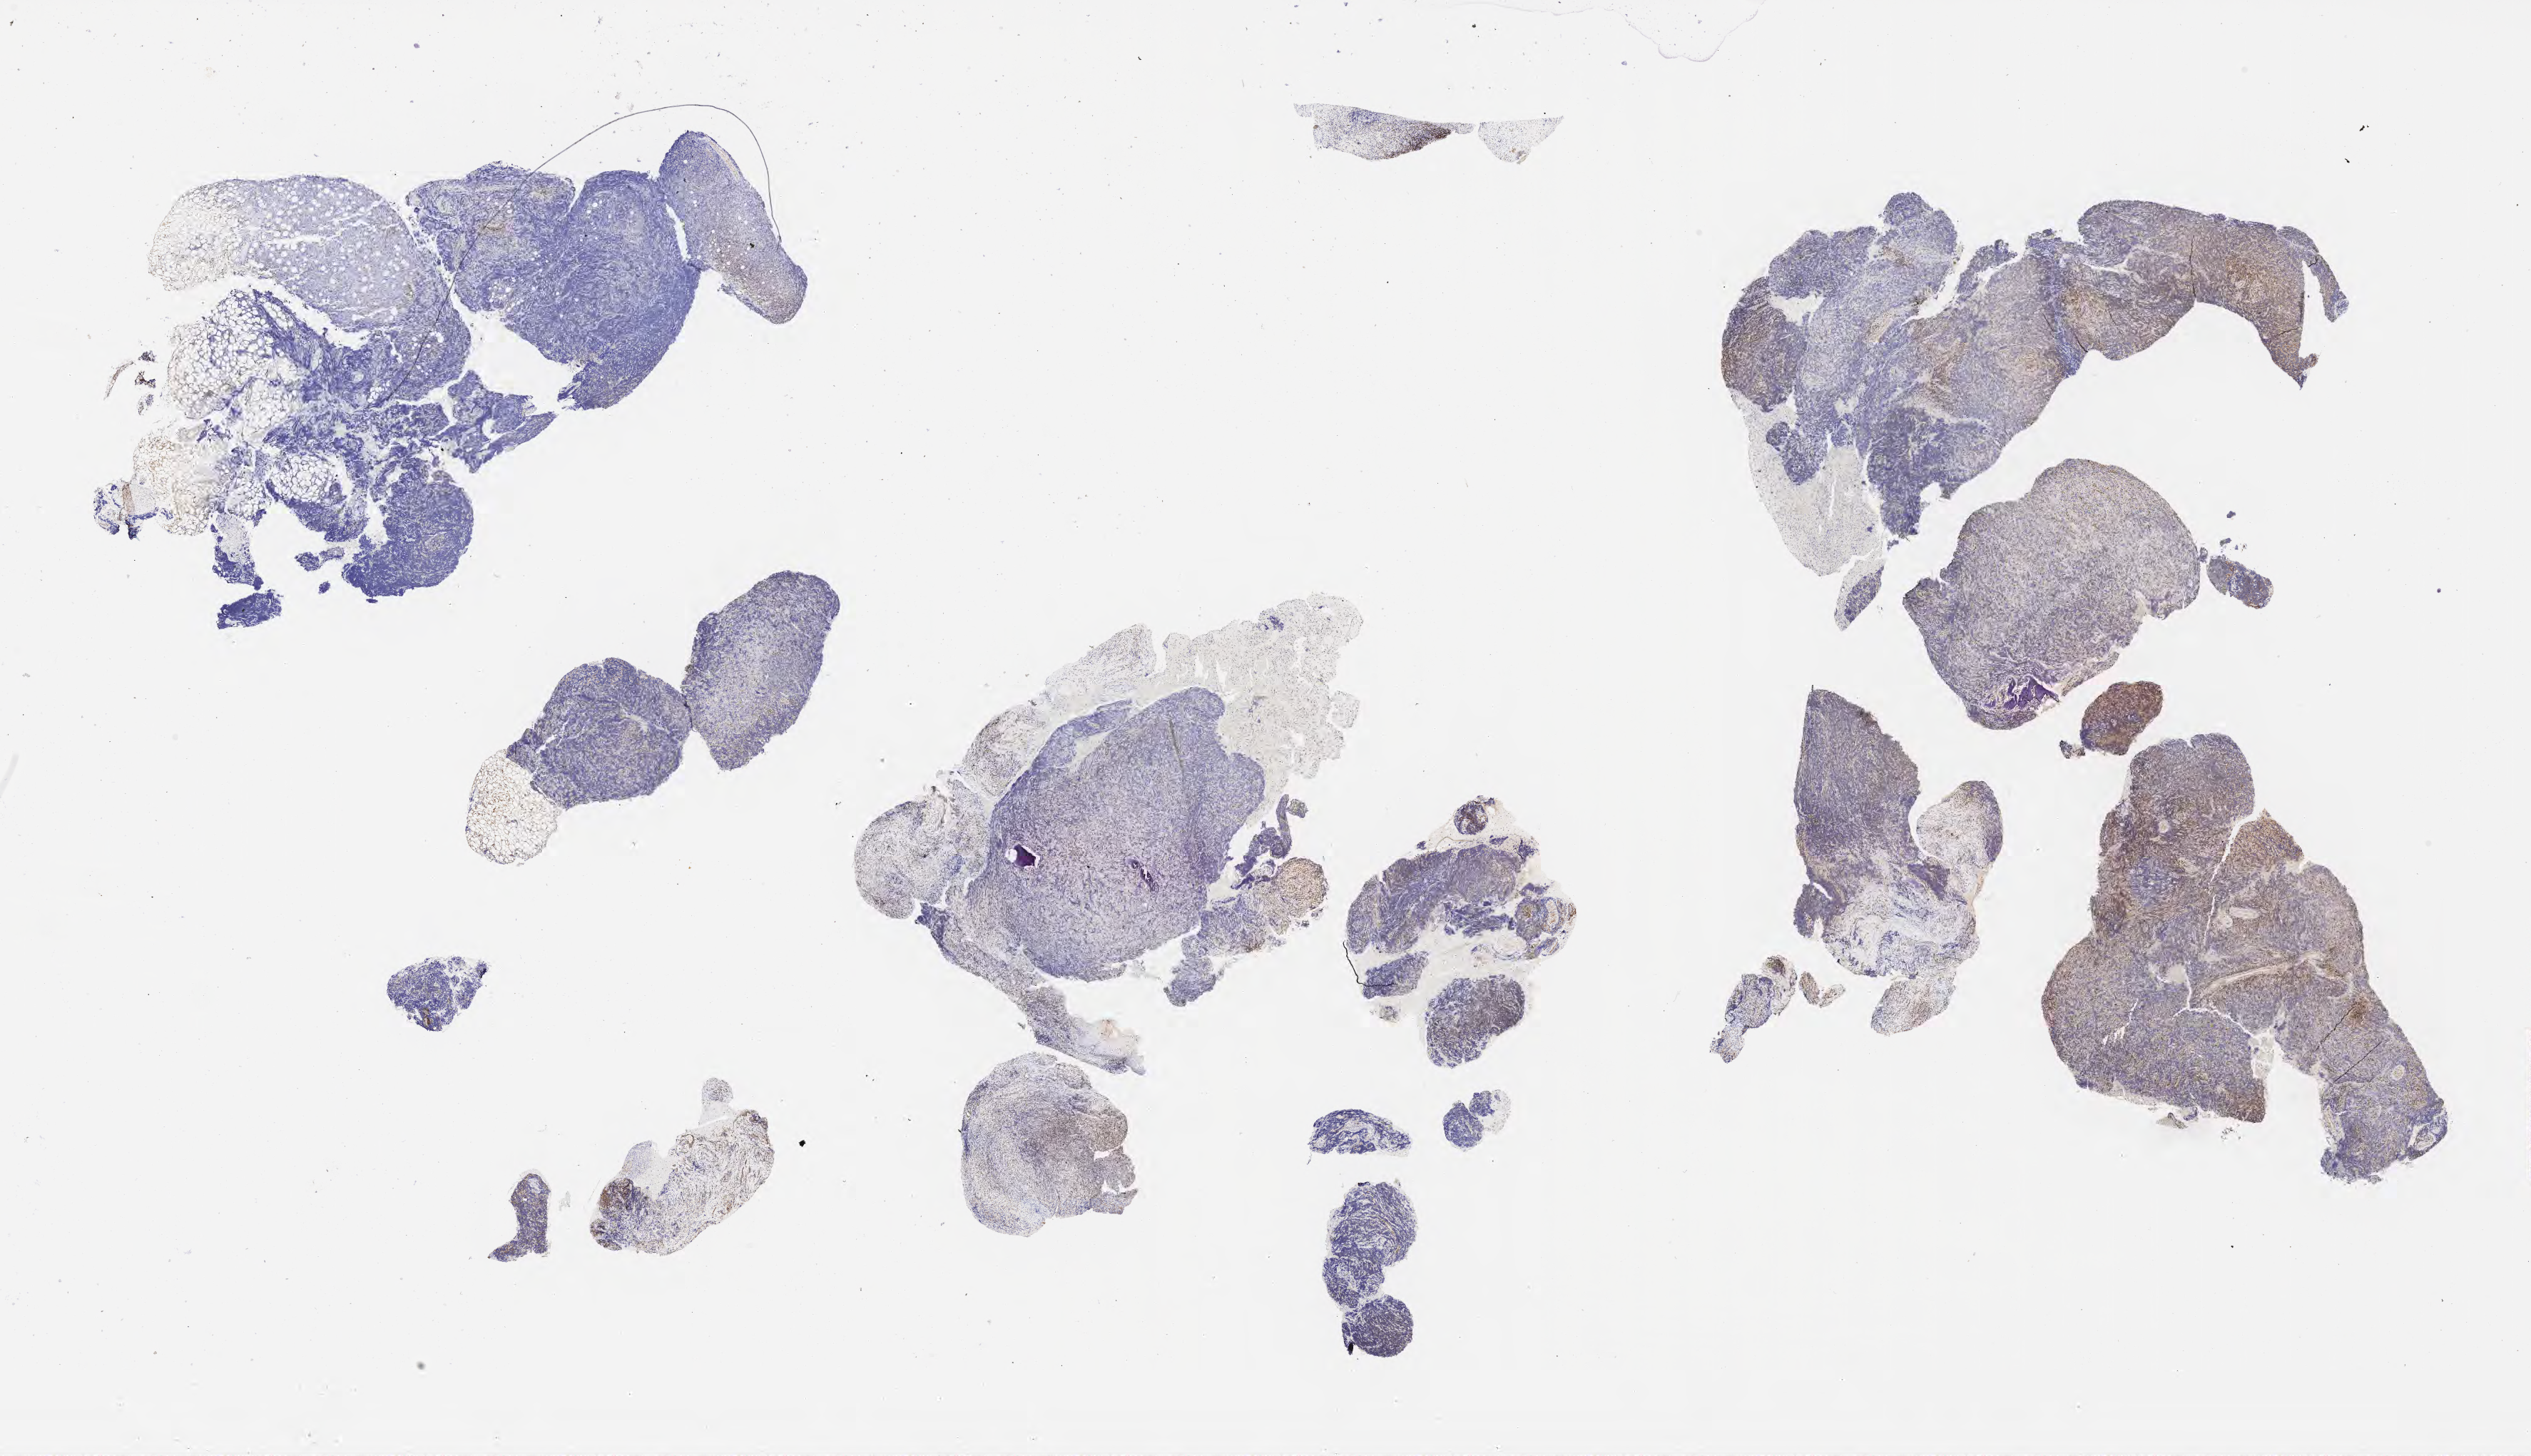
Whole-slide image, immunohistochemical stain for BCL2 — a low-resolution overview of the entire scanned area, about 28.7 x 16.5 mm; tumor tissue. Patient: male, age 45 years.
* diagnosis: Diffuse large B-cell lymphoma, NOS